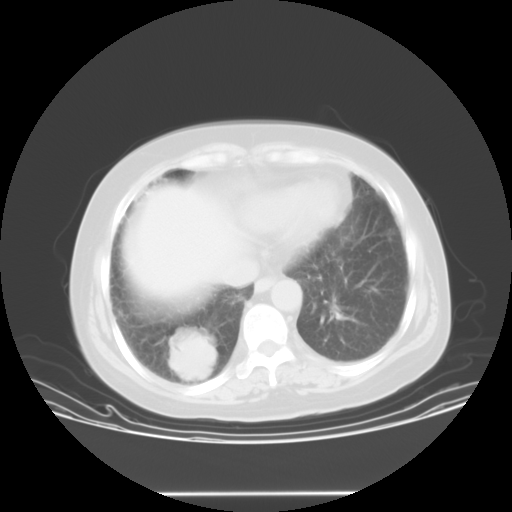
Chest CT, one axial slice. Slice 5 of 23 in the series (ordered by position). Reconstruction kernel STANDARD. Lung window (W 1500 / L -600 HU). 512 × 512 image matrix. Patient: female, 55 years. From the clinical record (not read from this slice): clinical TNM (as recorded): T2 N0 M1b.
Outlined on this slice (rectangle marked by the reading radiologist):
- lung tumour (recorded histology: squamous cell carcinoma): bounding box [x1, y1, x2, y2] px = [163, 326, 227, 398]